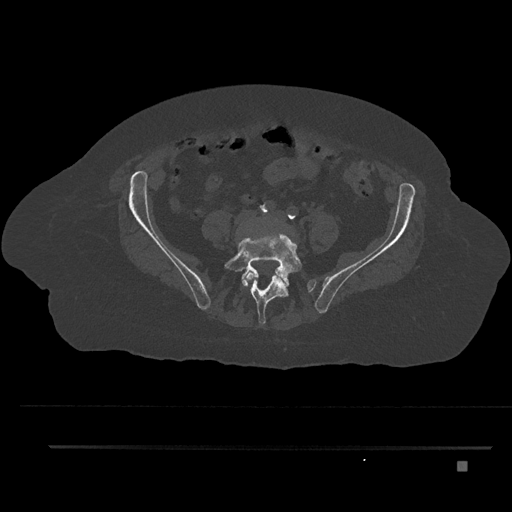
CT including the spine, one axial slice; slice 43 of 797 in the series (ordered by position); 120 kVp; bone window (W 1800 / L 400 HU); 512 × 512 image matrix, field of view 437 × 437 mm. Patient: female, 76 years. Case-level facts recorded for this patient, not image findings: primary cancer: lung; vertebrae with lytic lesions (as recorded): T11, L3.
Annotated regions visible in this slice (semi-automatic segmentation, software-assisted and operator-edited):
- L4 vertebra: bounding box (x1, y1, x2, y2) in pixels: (243, 268, 287, 285)
- L5 vertebra: (224, 231, 302, 325)